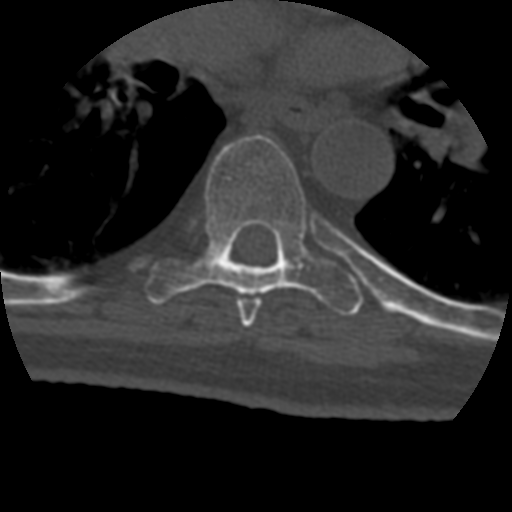
CT including the spine, one axial slice. Position 285 of 399 along the scan axis. Reconstruction kernel STANDARD. Bone window (W 1800 / L 400 HU). 512 × 512 image matrix, field of view 160 × 160 mm. Patient age 69 years. From the clinical record (not read from this slice): primary cancer: prostate.
Structures marked on this image (semi-automatically segmented with operator editing):
- T6 vertebra: bounding box (x1, y1, x2, y2) in pixels: (236, 297, 261, 328)
- T7 vertebra: (147, 135, 363, 316)